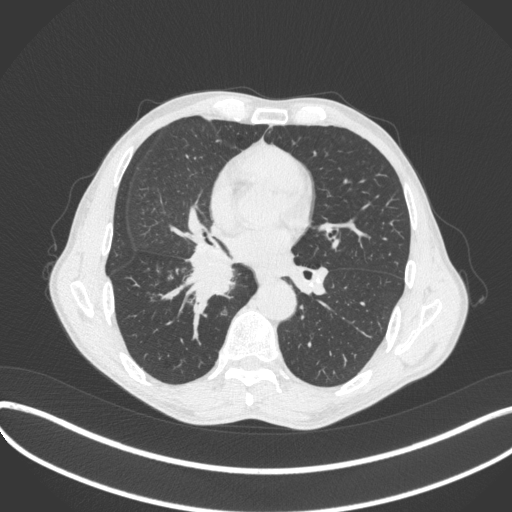
Chest CT, one axial slice. Position 213 of 481 along the scan axis. 120 kVp. Lung window (W 1500 / L -600 HU). 512 × 512 image matrix, field of view 400 × 400 mm. Male patient, age 65 years. From the clinical record (not read from this slice): clinical TNM (as recorded): T2a N0 M0; histopathological grade: G2.
Outlined on this slice (bounding box drawn by a radiologist):
- lung tumour (recorded histology: squamous cell carcinoma): bounding box [x1, y1, x2, y2] px = [182, 241, 242, 303]